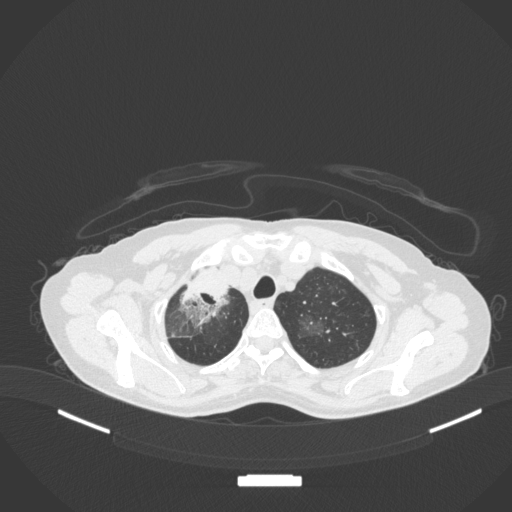
Chest CT, one axial slice. Slice 277 of 311 in the series (ordered by position). 120 kVp. Lung window (W 1500 / L -600 HU). 1 mm slice thickness. 512 × 512 image matrix. Patient: female, 59 years. From the clinical record (not read from this slice): clinical TNM (as recorded): T3 N0 M0; histopathological grade: G1.
Structures marked on this image (bounding box drawn by a radiologist):
- lung tumour (recorded histology: adenocarcinoma): bounding box (x1, y1, x2, y2) in pixels: (177, 278, 222, 327)